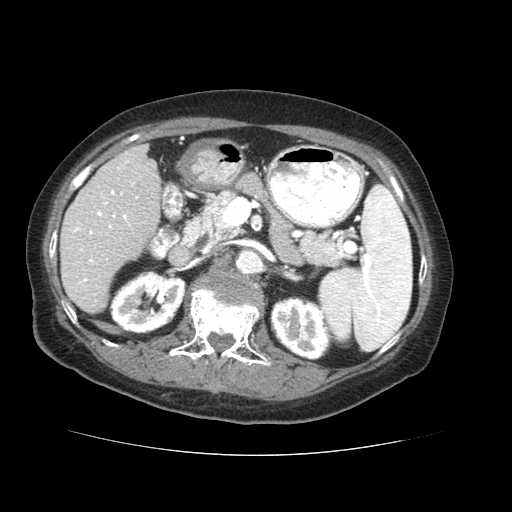
Contrast-enhanced abdominal CT (liver protocol), one axial slice; slice 21 of 73 in the series (ordered by position); reconstruction kernel STANDARD; 120 kVp; soft-tissue window (W 400 / L 40 HU); 2.5 mm slice thickness; 512 × 512 image matrix, field of view 360 × 360 mm. From the clinical record (not read from this slice): diagnosis: hepatocellular carcinoma (patient treated with transarterial chemoembolisation; whether this scan precedes or follows treatment is not stated here); TNM stage (as recorded): Stage-IVB.
Annotated regions visible in this slice (semi-automatic segmentation, software-assisted and operator-edited):
- liver parenchyma outside the tumour (the mass and vessels are separate outlines, so this box may not span the whole liver): bounding box [x1, y1, x2, y2] px = [60, 144, 160, 312]
- liver vessels: [64, 160, 138, 295]